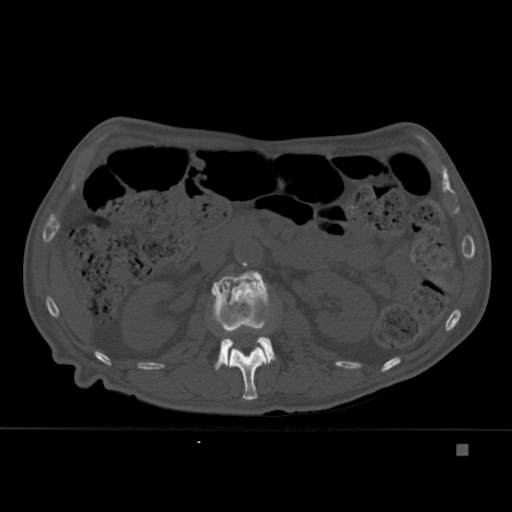
CT including the spine, one axial slice; slice 173 of 451 in the series (ordered by position); bone window (W 1800 / L 400 HU); 512 × 512 image matrix. Patient: male, 75 years. From the clinical record (not read from this slice): primary cancer: prostate.
Outlined on this slice (semi-automatically segmented with operator editing):
- L1 vertebra: bounding box (x1, y1, x2, y2) in pixels: (222, 326, 268, 400)
- L2 vertebra: (211, 270, 276, 370)